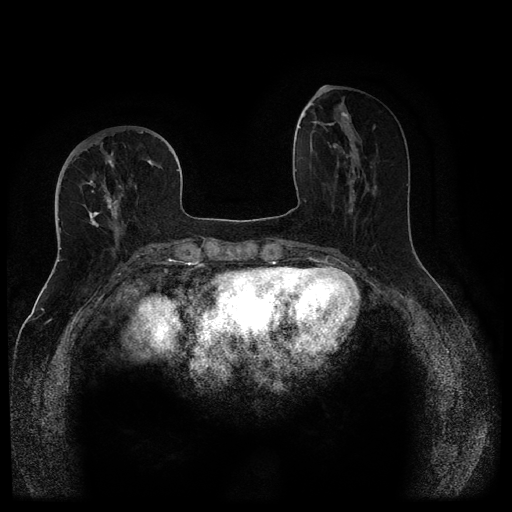
Breast MRI (dynamic contrast-enhanced, multi-phase), one axial slice; position 41 of 116 along the scan axis; dynamic contrast-enhanced series, time point 2 of 5 at this slice position (early post-contrast); 1.5 T; TE 2.6 ms, TR 5.4 ms; 2 mm slice thickness; 512 × 512 image matrix, field of view 340 × 340 mm. Patient: female, 68 years.
Outlined on this slice (semi-automatically segmented with operator editing):
- breast lesion (labelled benign in the annotation): box from (x=337, y=111) to (x=350, y=124) px